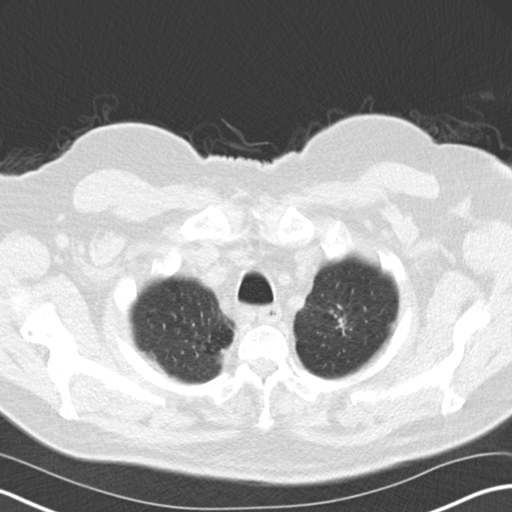
Axial slice from a low-dose chest CT screening exam; third screening round (two years after baseline); lung window (W 1500 / L -600 HU); standard (soft-tissue) reconstruction kernel (B30f); slice 10 of 69 in the series. Male participant, aged 67 years at enrolment. Former smoker at enrolment.
Expert reader's lesion annotation, bounding box [x1, y1, x2, y2] px = [318, 301, 362, 342]. Reader record for this screening exam (exam-level; its link to the box is not recorded): non-calcified nodule or mass ≥4 mm, left upper lobe, 20 × 15 mm, spiculated (stellate) margins, soft tissue attenuation, pre-existing on the prior screen: yes; interval growth: yes. Participant outcome: lung cancer diagnosed 52 days after this screen — adenocarcinoma, NOS, left upper lobe, moderately differentiated (G2), stage IIA (AJCC 6th edition), 18 mm at pathology.